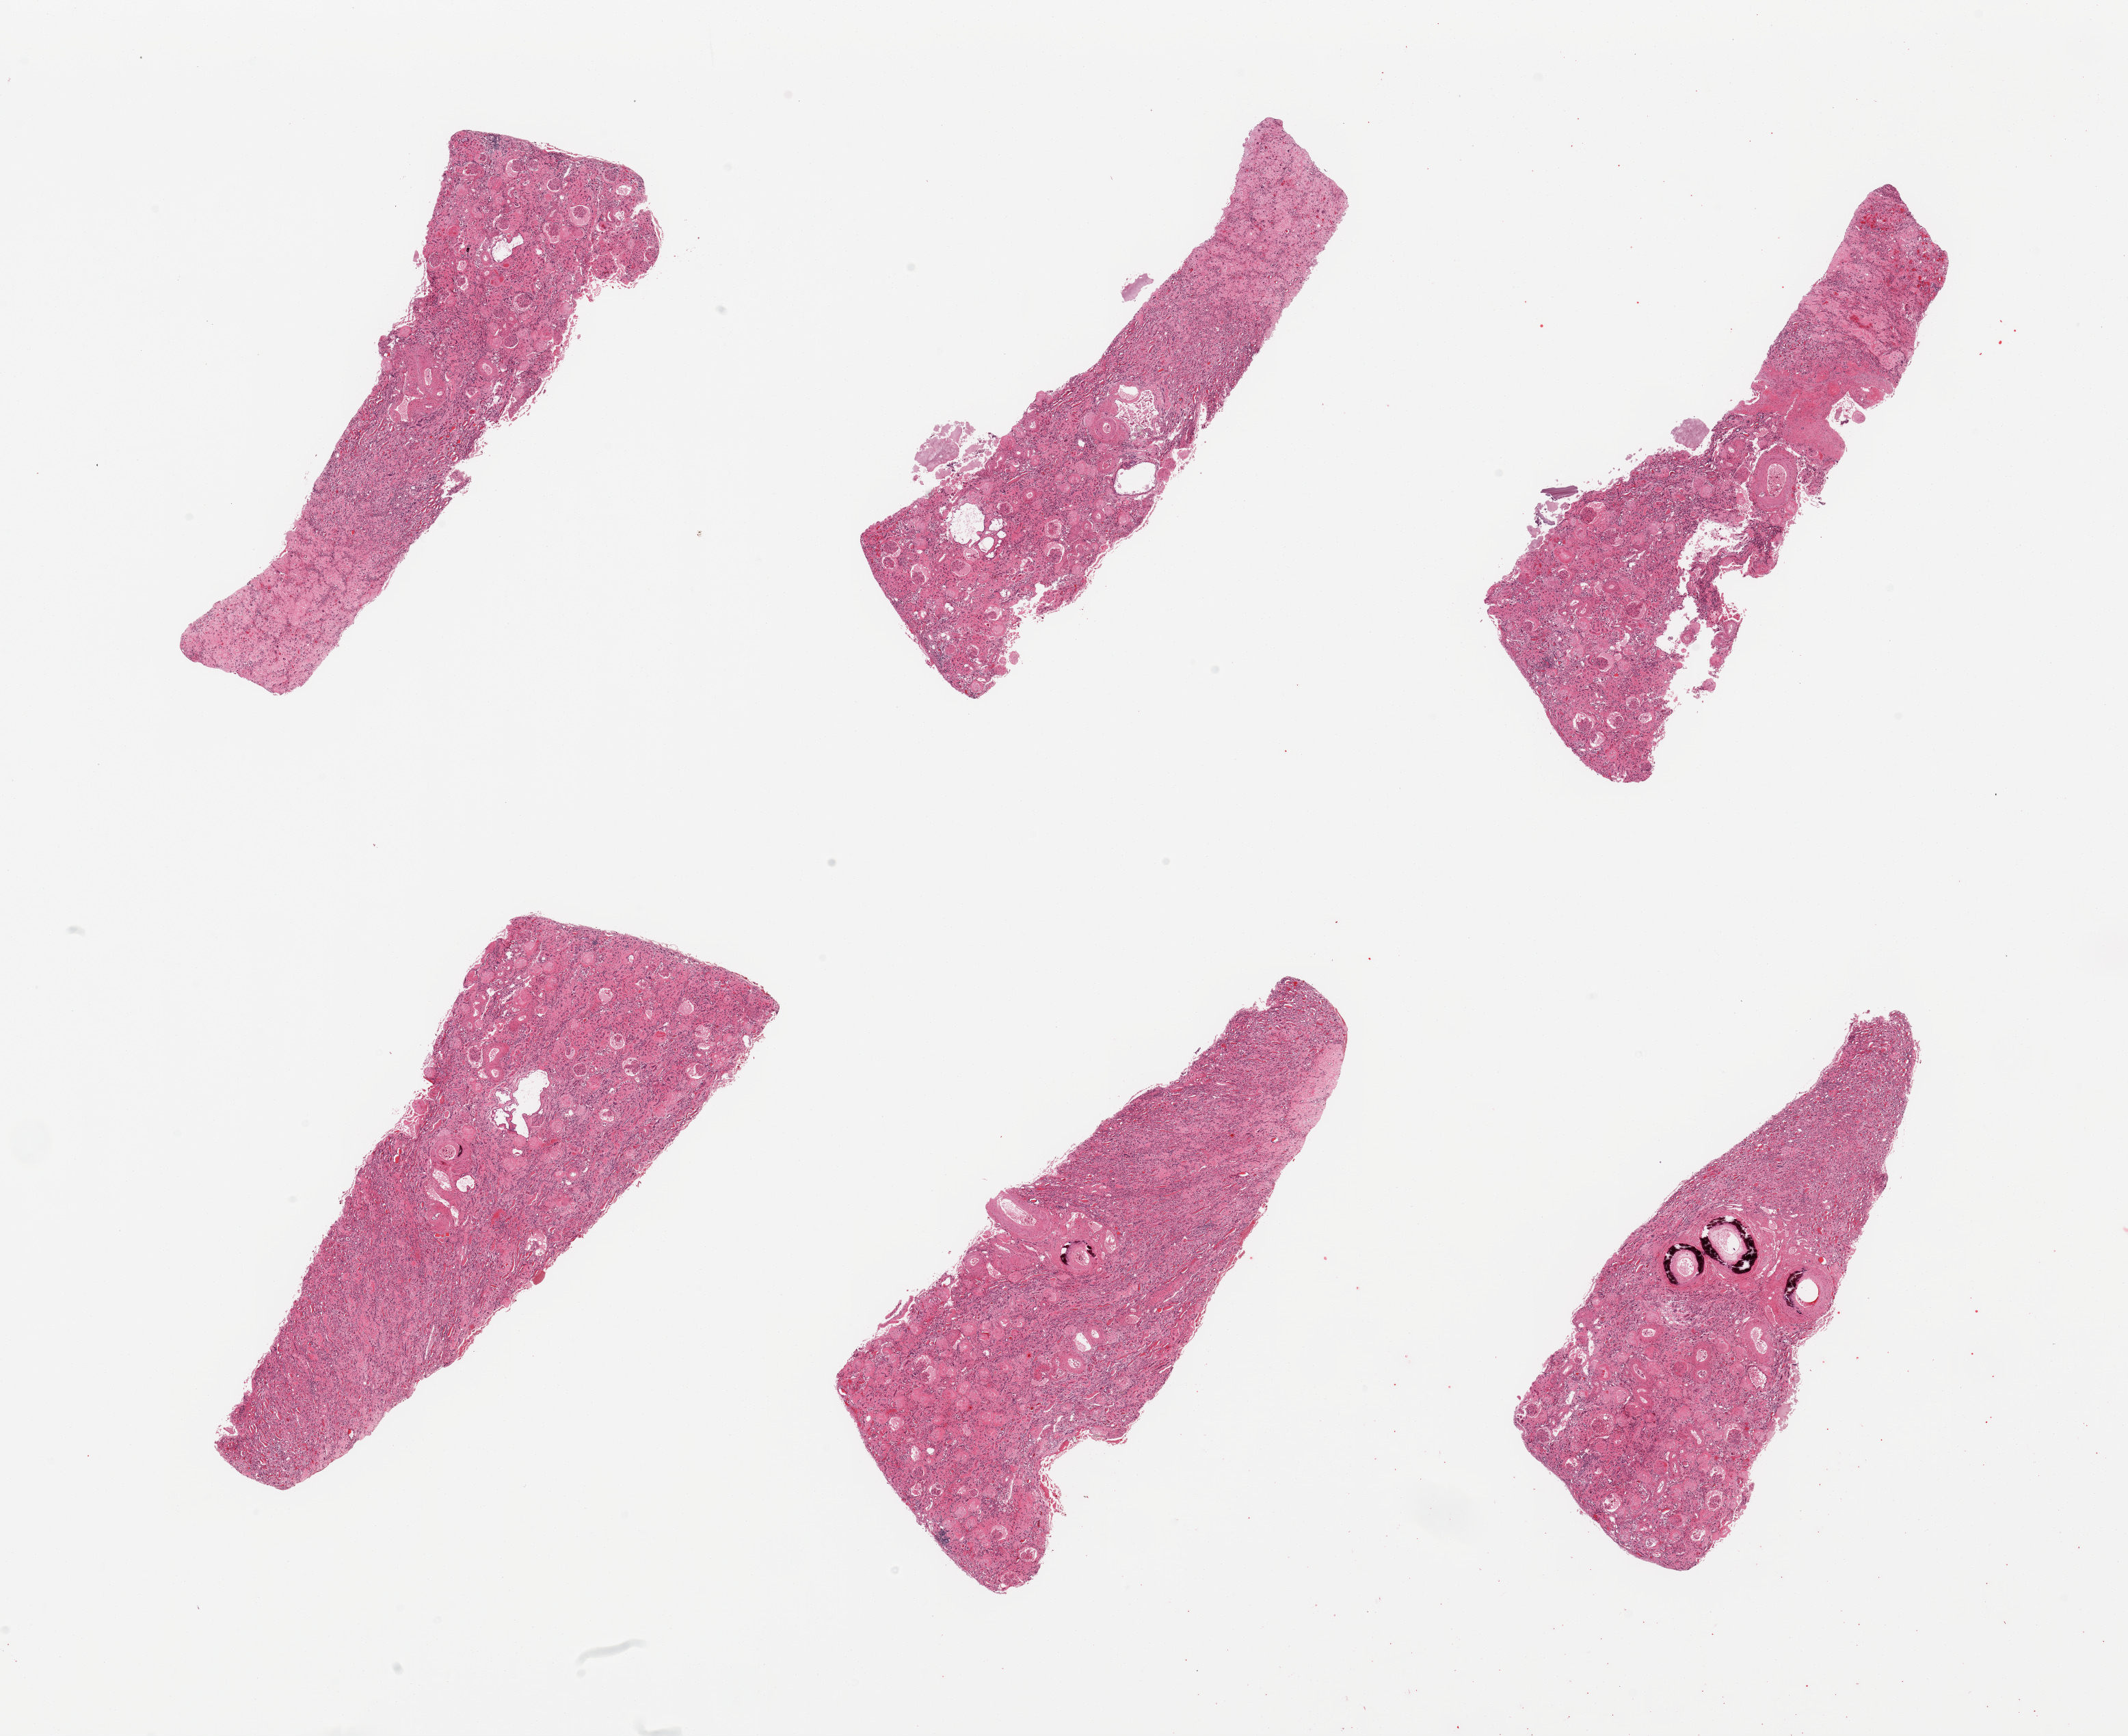
Whole-slide image, haematoxylin and eosin stain, low-resolution overview of the scanned area, about 24.6 x 20.1 mm, PAXgene-fixed paraffin-embedded (PFPE) section, section of renal cortex (target tissue), donor tissue sample. Donor: male.
Reviewer comment on this tissue sample: 6 pieces; severe vascular, glomerular & interstitial sclerosis; hyalin casts; calcified arteries; consistent with end stage renal disease.